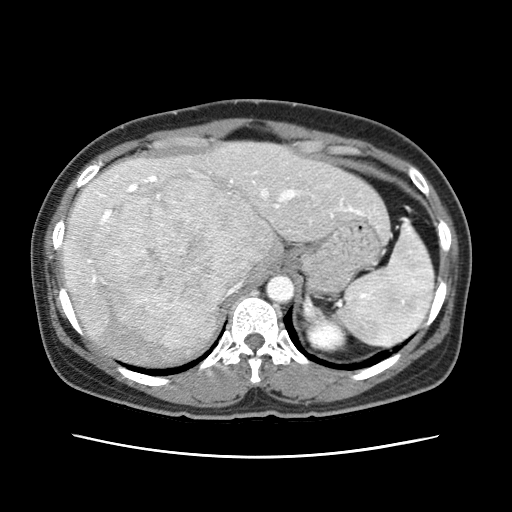
Contrast-enhanced abdominal CT (liver protocol), one axial slice; slice 47 of 79 in the series (ordered by position); soft-tissue window (W 400 / L 40 HU); 2.5 mm slice thickness; 512 × 512 image matrix, field of view 340 × 340 mm. From the clinical record (not read from this slice): diagnosis: hepatocellular carcinoma (patient treated with transarterial chemoembolisation; whether this scan precedes or follows treatment is not stated here); TNM stage (as recorded): Stage-I; Child-Pugh class: A.
Annotated regions visible in this slice (semi-automatic segmentation, software-assisted and operator-edited):
- abdominal aorta: bounding box <266,276,294,301> (left, top, right, bottom; pixels)
- liver parenchyma outside the tumour (the mass and vessels are separate outlines, so this box may not span the whole liver): <60,142,380,364>
- mass: <99,178,272,347>
- liver vessels: <73,172,363,282>